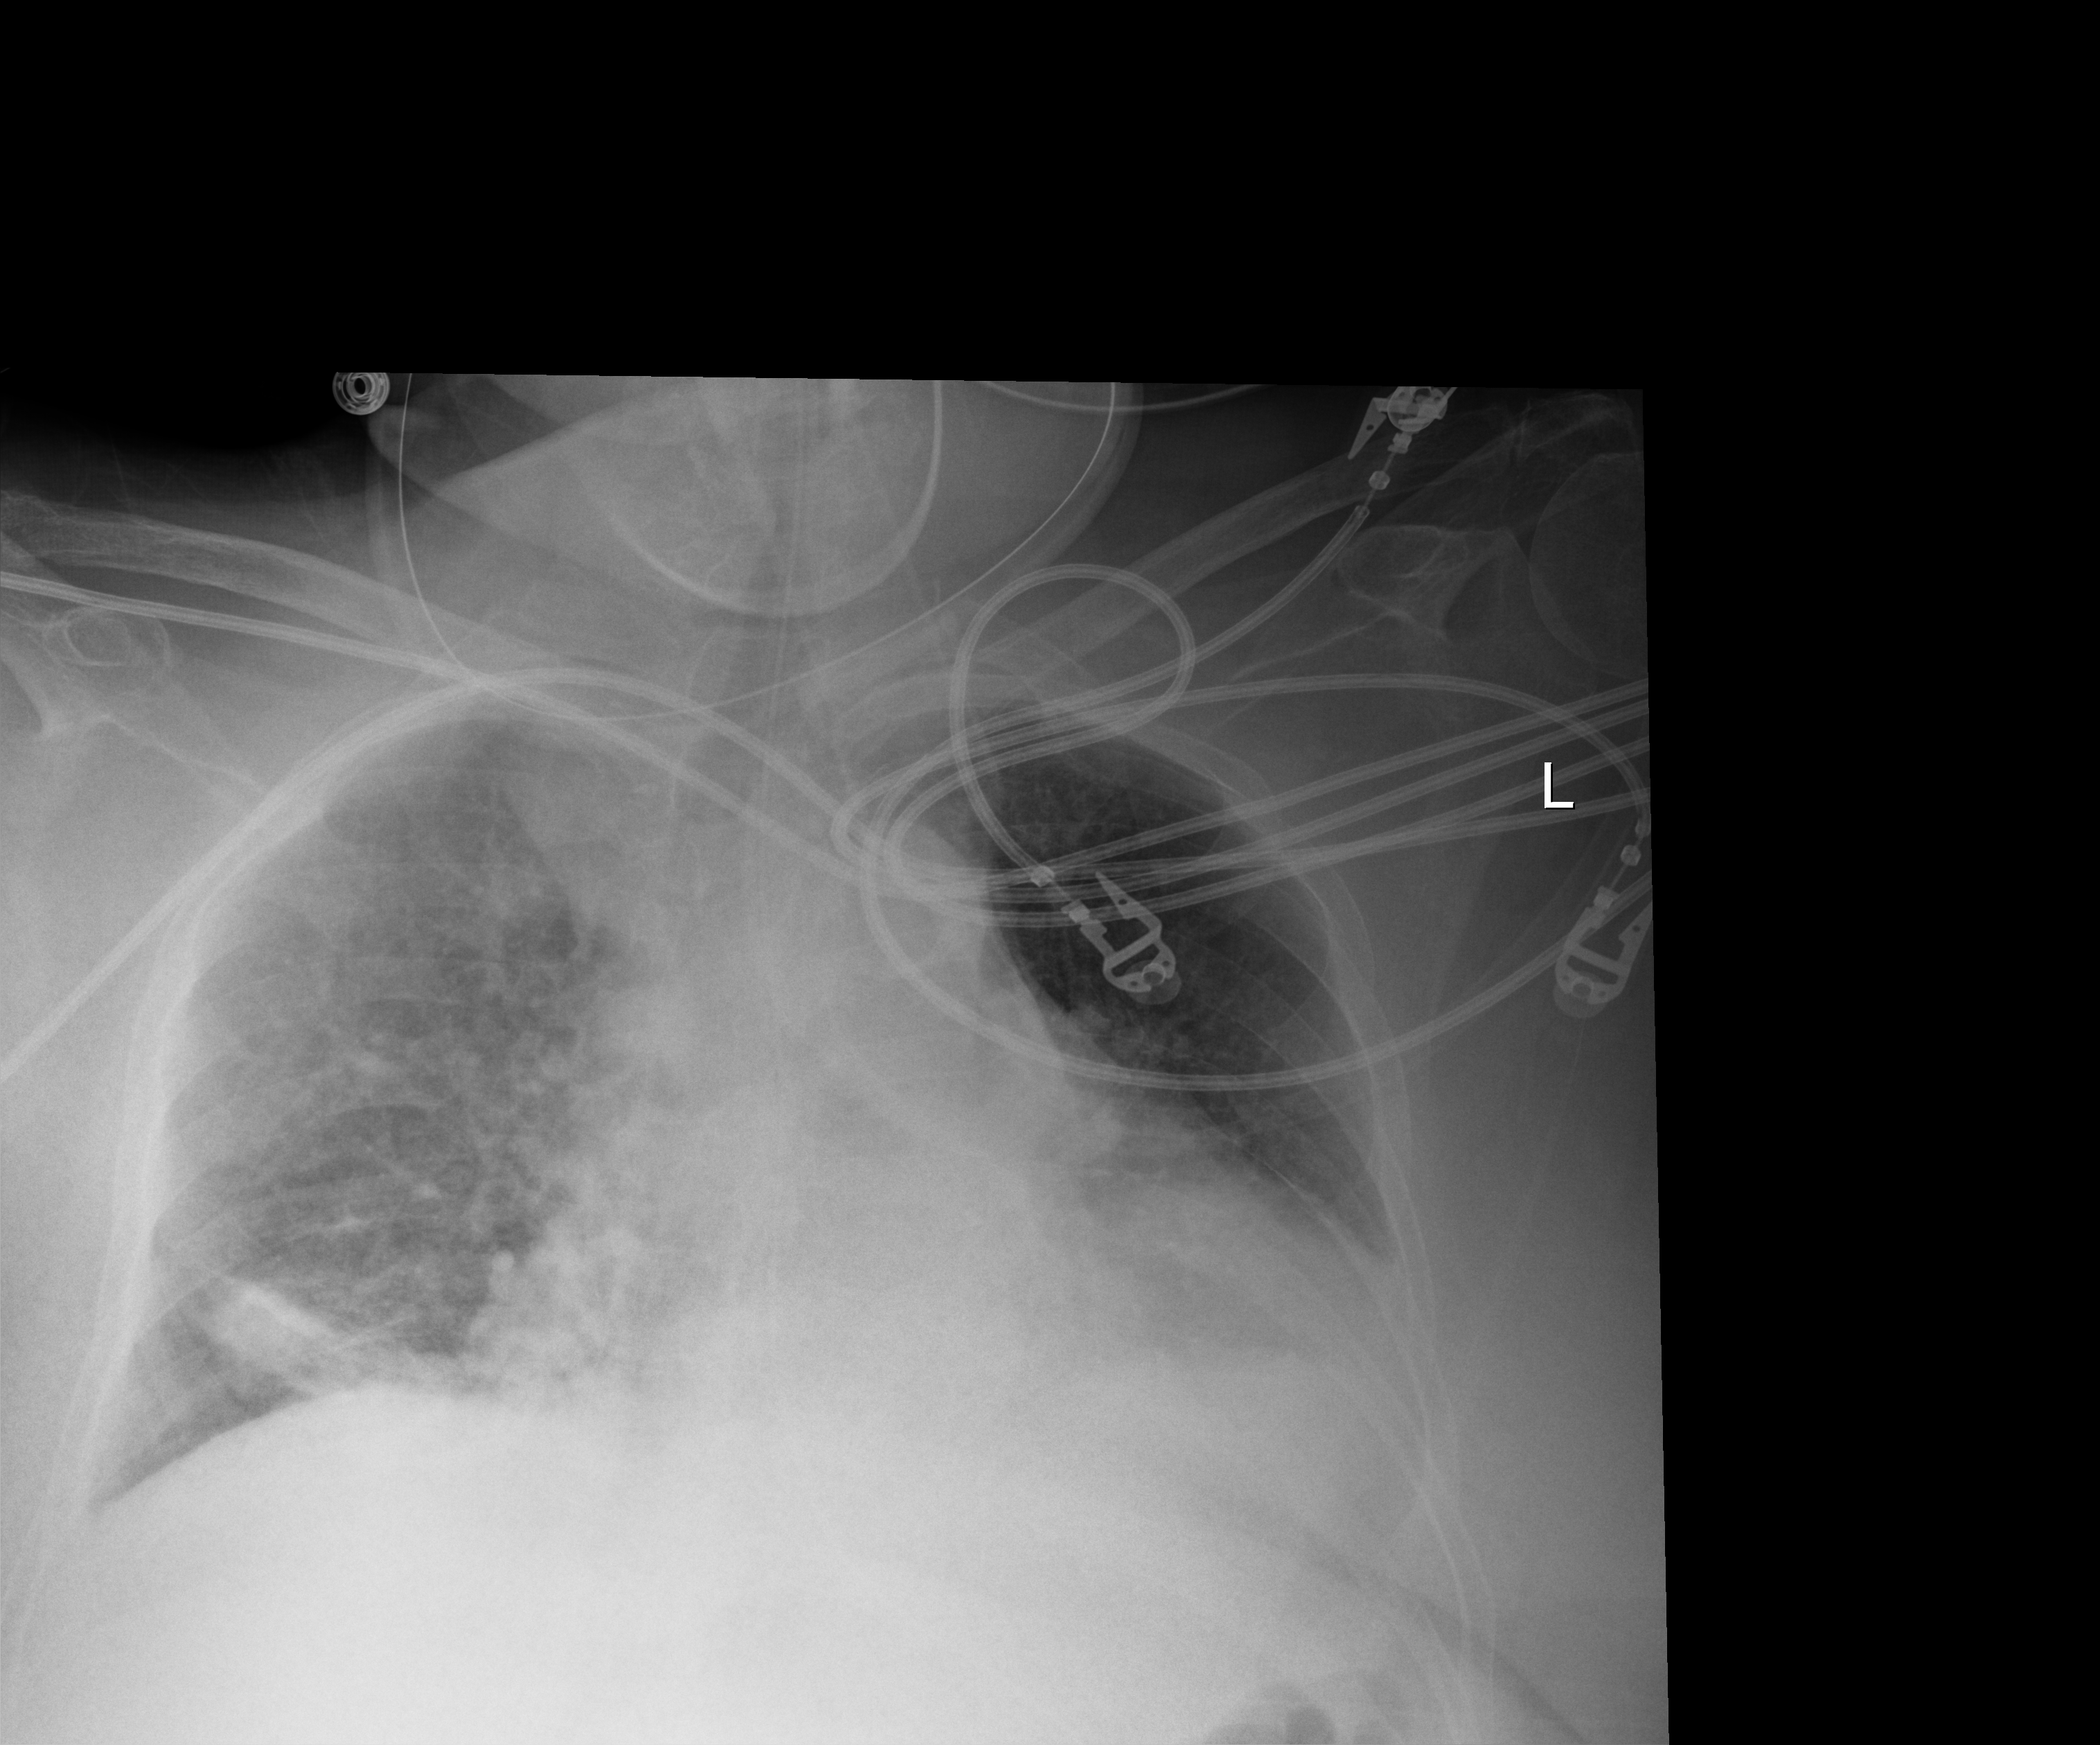
Portable chest radiograph; anteroposterior (AP) projection. Patient hospitalised with COVID-19; female, aged 60–74 years.
Admission-level facts for this patient (not findings on this image; timing relative to this image not recorded): admitted to intensive care during this hospital stay: yes; mechanically ventilated during this hospital stay: no.